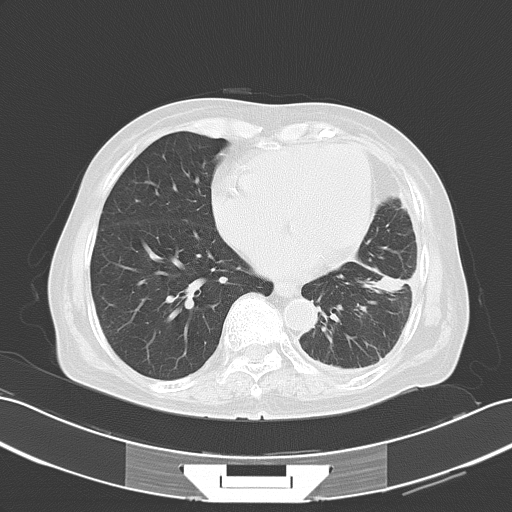
Chest CT, one axial slice. Slice 23 of 60 in the series (ordered by position). Reconstruction kernel B70f. Lung window (W 1500 / L -600 HU). 5 mm slice thickness. 512 × 512 image matrix. Patient: female, 82 years. Case-level facts recorded for this patient, not image findings: clinical TNM (as recorded): T1c N0 M1.
Outlined on this slice (rectangle marked by the reading radiologist):
- lung tumour (recorded histology: adenocarcinoma): bounding box <362,265,412,306> (left, top, right, bottom; pixels)